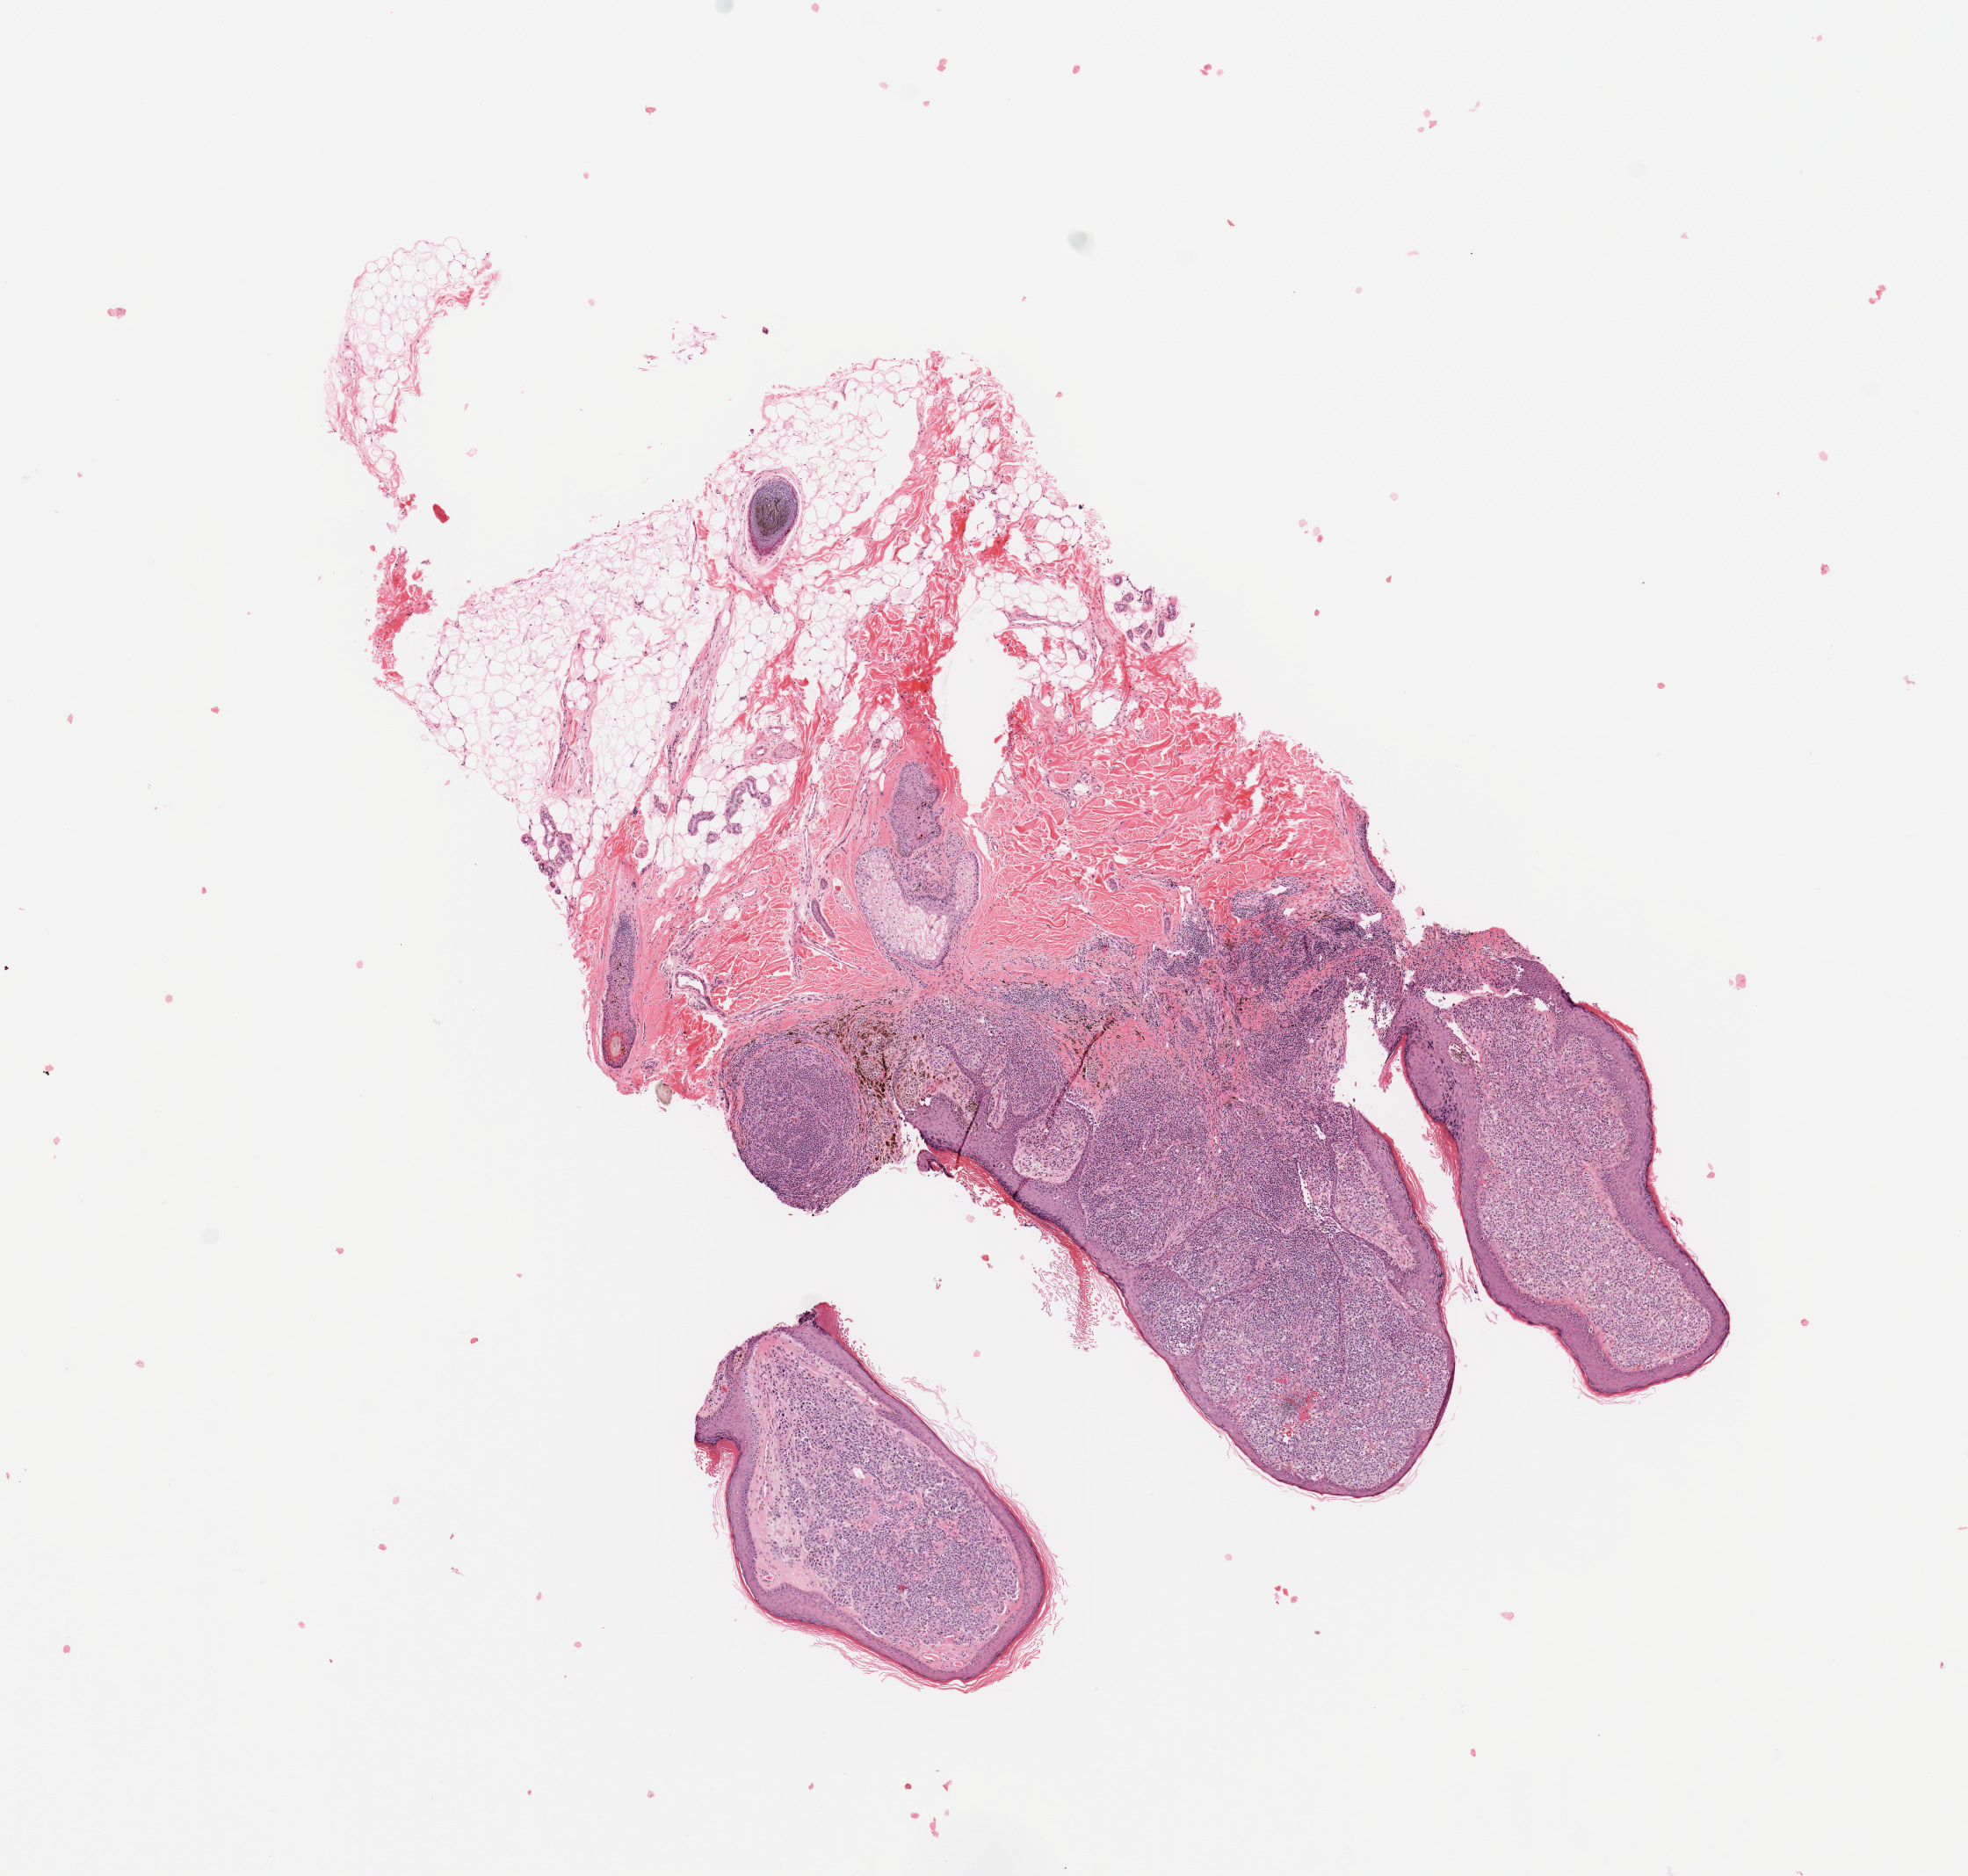
Digitized Hematoxylin and eosin (H&E) stained tissue section (whole slide), low-resolution overview of the scanned area, about 8.9 x 8.4 mm, melanoma tumour tissue; sampled site not recorded. 73-year-old female patient.
Histologic diagnosis: Malignant melanoma, NOS. AJCC pathologic stage: IIA. Primary tumour site (as recorded): head & neck.